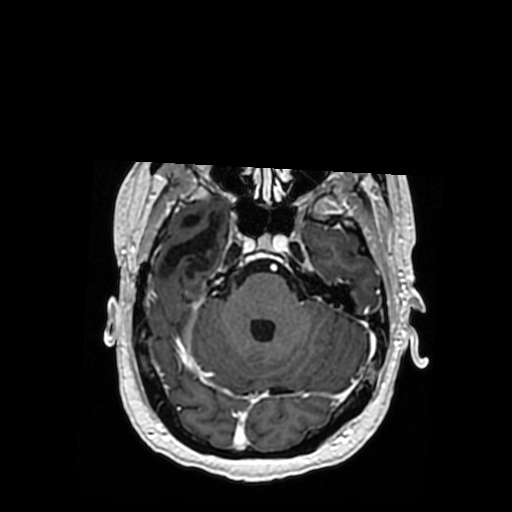
Brain MRI from a brain-tumour surgery series, one axial slice; slice 246 of 364 in the series (ordered by position); T1-weighted post-contrast; 0.5 mm slice thickness; 512 × 512 image matrix, field of view 260 × 260 mm. From the clinical record (not read from this slice): histopathology: Oligodendroglioma; WHO grade: 3; IDH mutation: yes.
Structures marked on this image (expert manual segmentation):
- previous resection cavity: bounding box (x1, y1, x2, y2) in pixels: (161, 215, 219, 277)